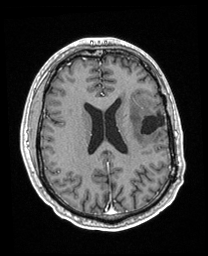
Brain MRI from a brain-tumour surgery series, one axial slice. Position 89 of 208 along the scan axis. T1-weighted post-contrast. 1 mm slice thickness. 208 × 256 image matrix, field of view 211 × 260 mm. Case-level facts recorded for this patient, not image findings: histopathology: Astrocytoma; WHO grade: 3; IDH mutation: yes; tumour location: Left Insular.
Annotated regions visible in this slice (manually delineated by an expert):
- previous resection cavity: bounding box <141,112,165,135> (left, top, right, bottom; pixels)